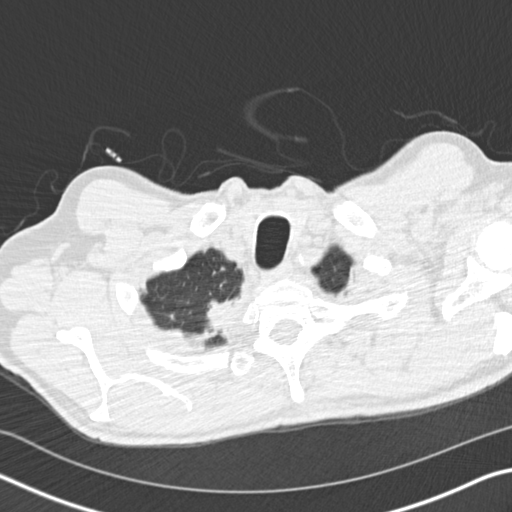
Low-dose screening chest CT, one axial slice; position 161 of 175 along the scan axis; lung window (W 1500 / L -600 HU); 512 × 512 image matrix, field of view 340 × 340 mm.
Outlined on this slice (expert manual segmentation):
- lesion 1 (tumor, upper lobe of right lung): bounding box [x1, y1, x2, y2] px = [207, 297, 245, 337]